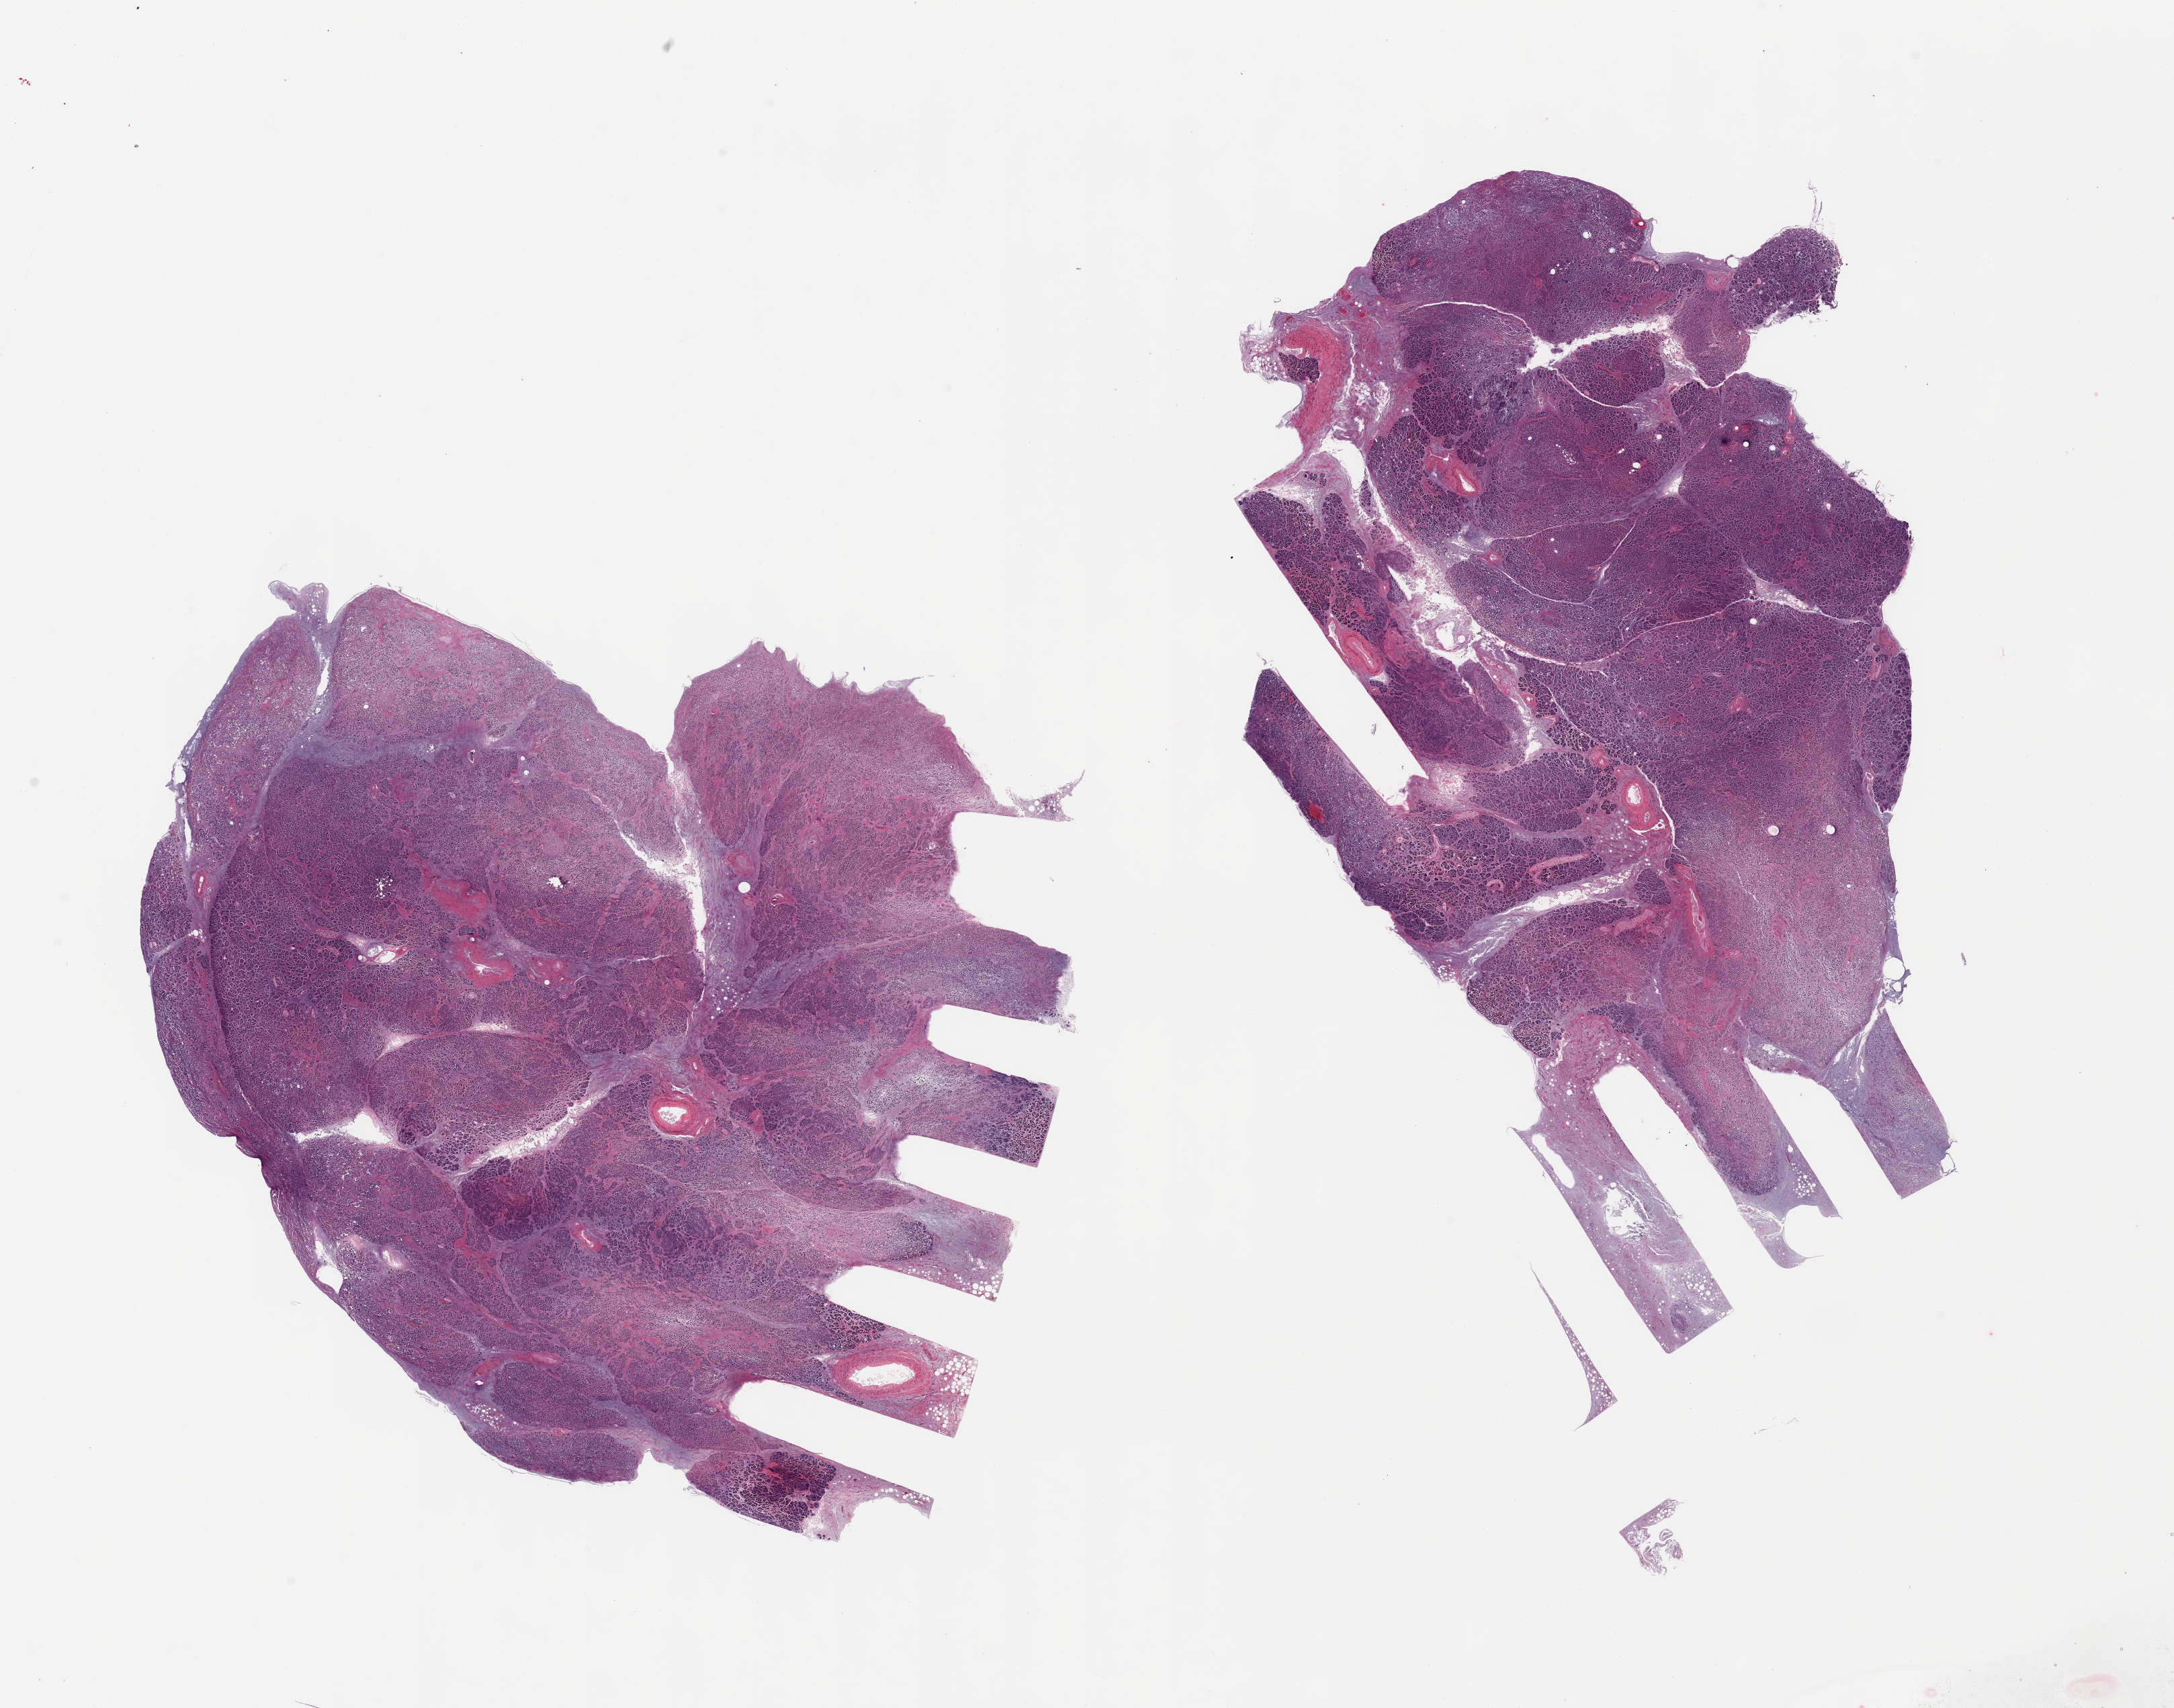
H&E whole-slide image — whole scanned area (about 25.6 x 20.1 mm) shown as a low-resolution overview, PAXgene-fixed, paraffin-embedded tissue, section of pancreas (target tissue), tissue donor sample. Donor sex: male.
• review note (as recorded): 2 pieces; severely autolyzed pancreas